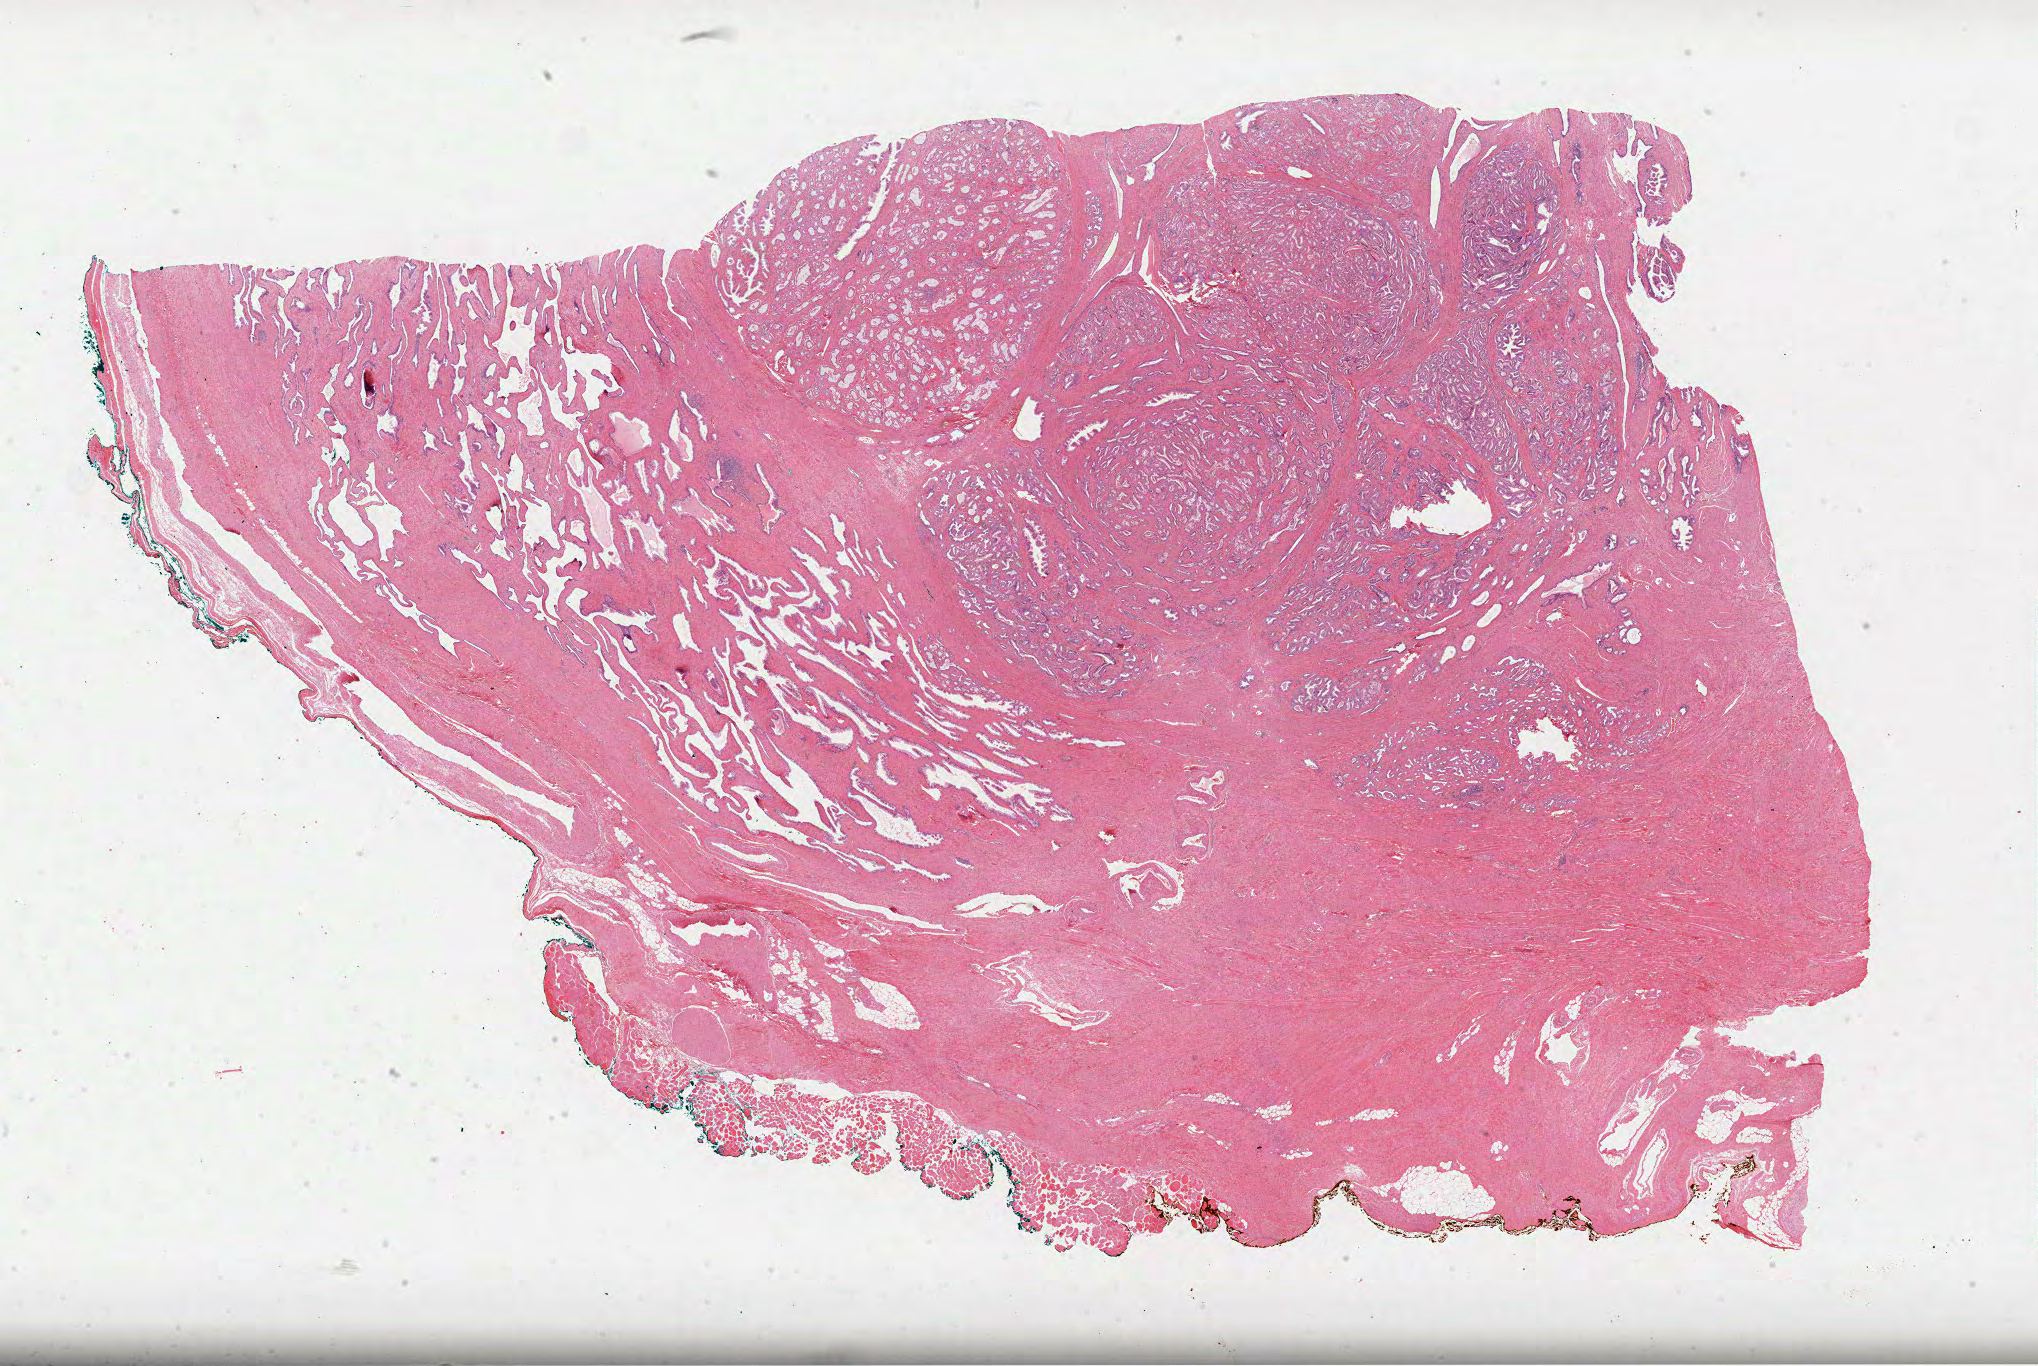
Whole-slide histology image, H&E-stained — a low-resolution overview of the entire scanned area, about 32.9 x 22.0 mm (slide scanned at 40x); formalin-fixed paraffin-embedded (FFPE) diagnostic section; primary tumour sample from the prostate. Male, age 71 years at initial diagnosis. Gleason score: 7 (3+4).
Laterality: bilateral. Diagnosis: Acinar cell carcinoma (prostate gland).